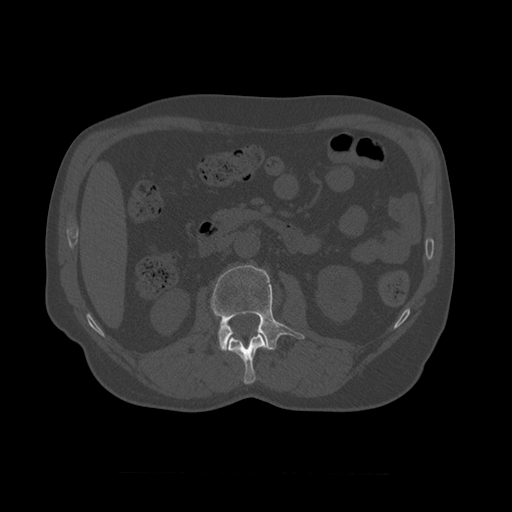
CT including the spine, one axial slice. Slice 339 of 450 in the series (ordered by position). Bone window (W 1800 / L 400 HU). 1.25 mm slice thickness. 512 × 512 image matrix. Patient age 75 years. From the clinical record (not read from this slice): primary cancer: prostate.
Structures marked on this image (semi-automatic segmentation, software-assisted and operator-edited):
- L1 vertebra: bounding box [x1, y1, x2, y2] px = [227, 331, 269, 385]
- L2 vertebra: [211, 265, 305, 353]